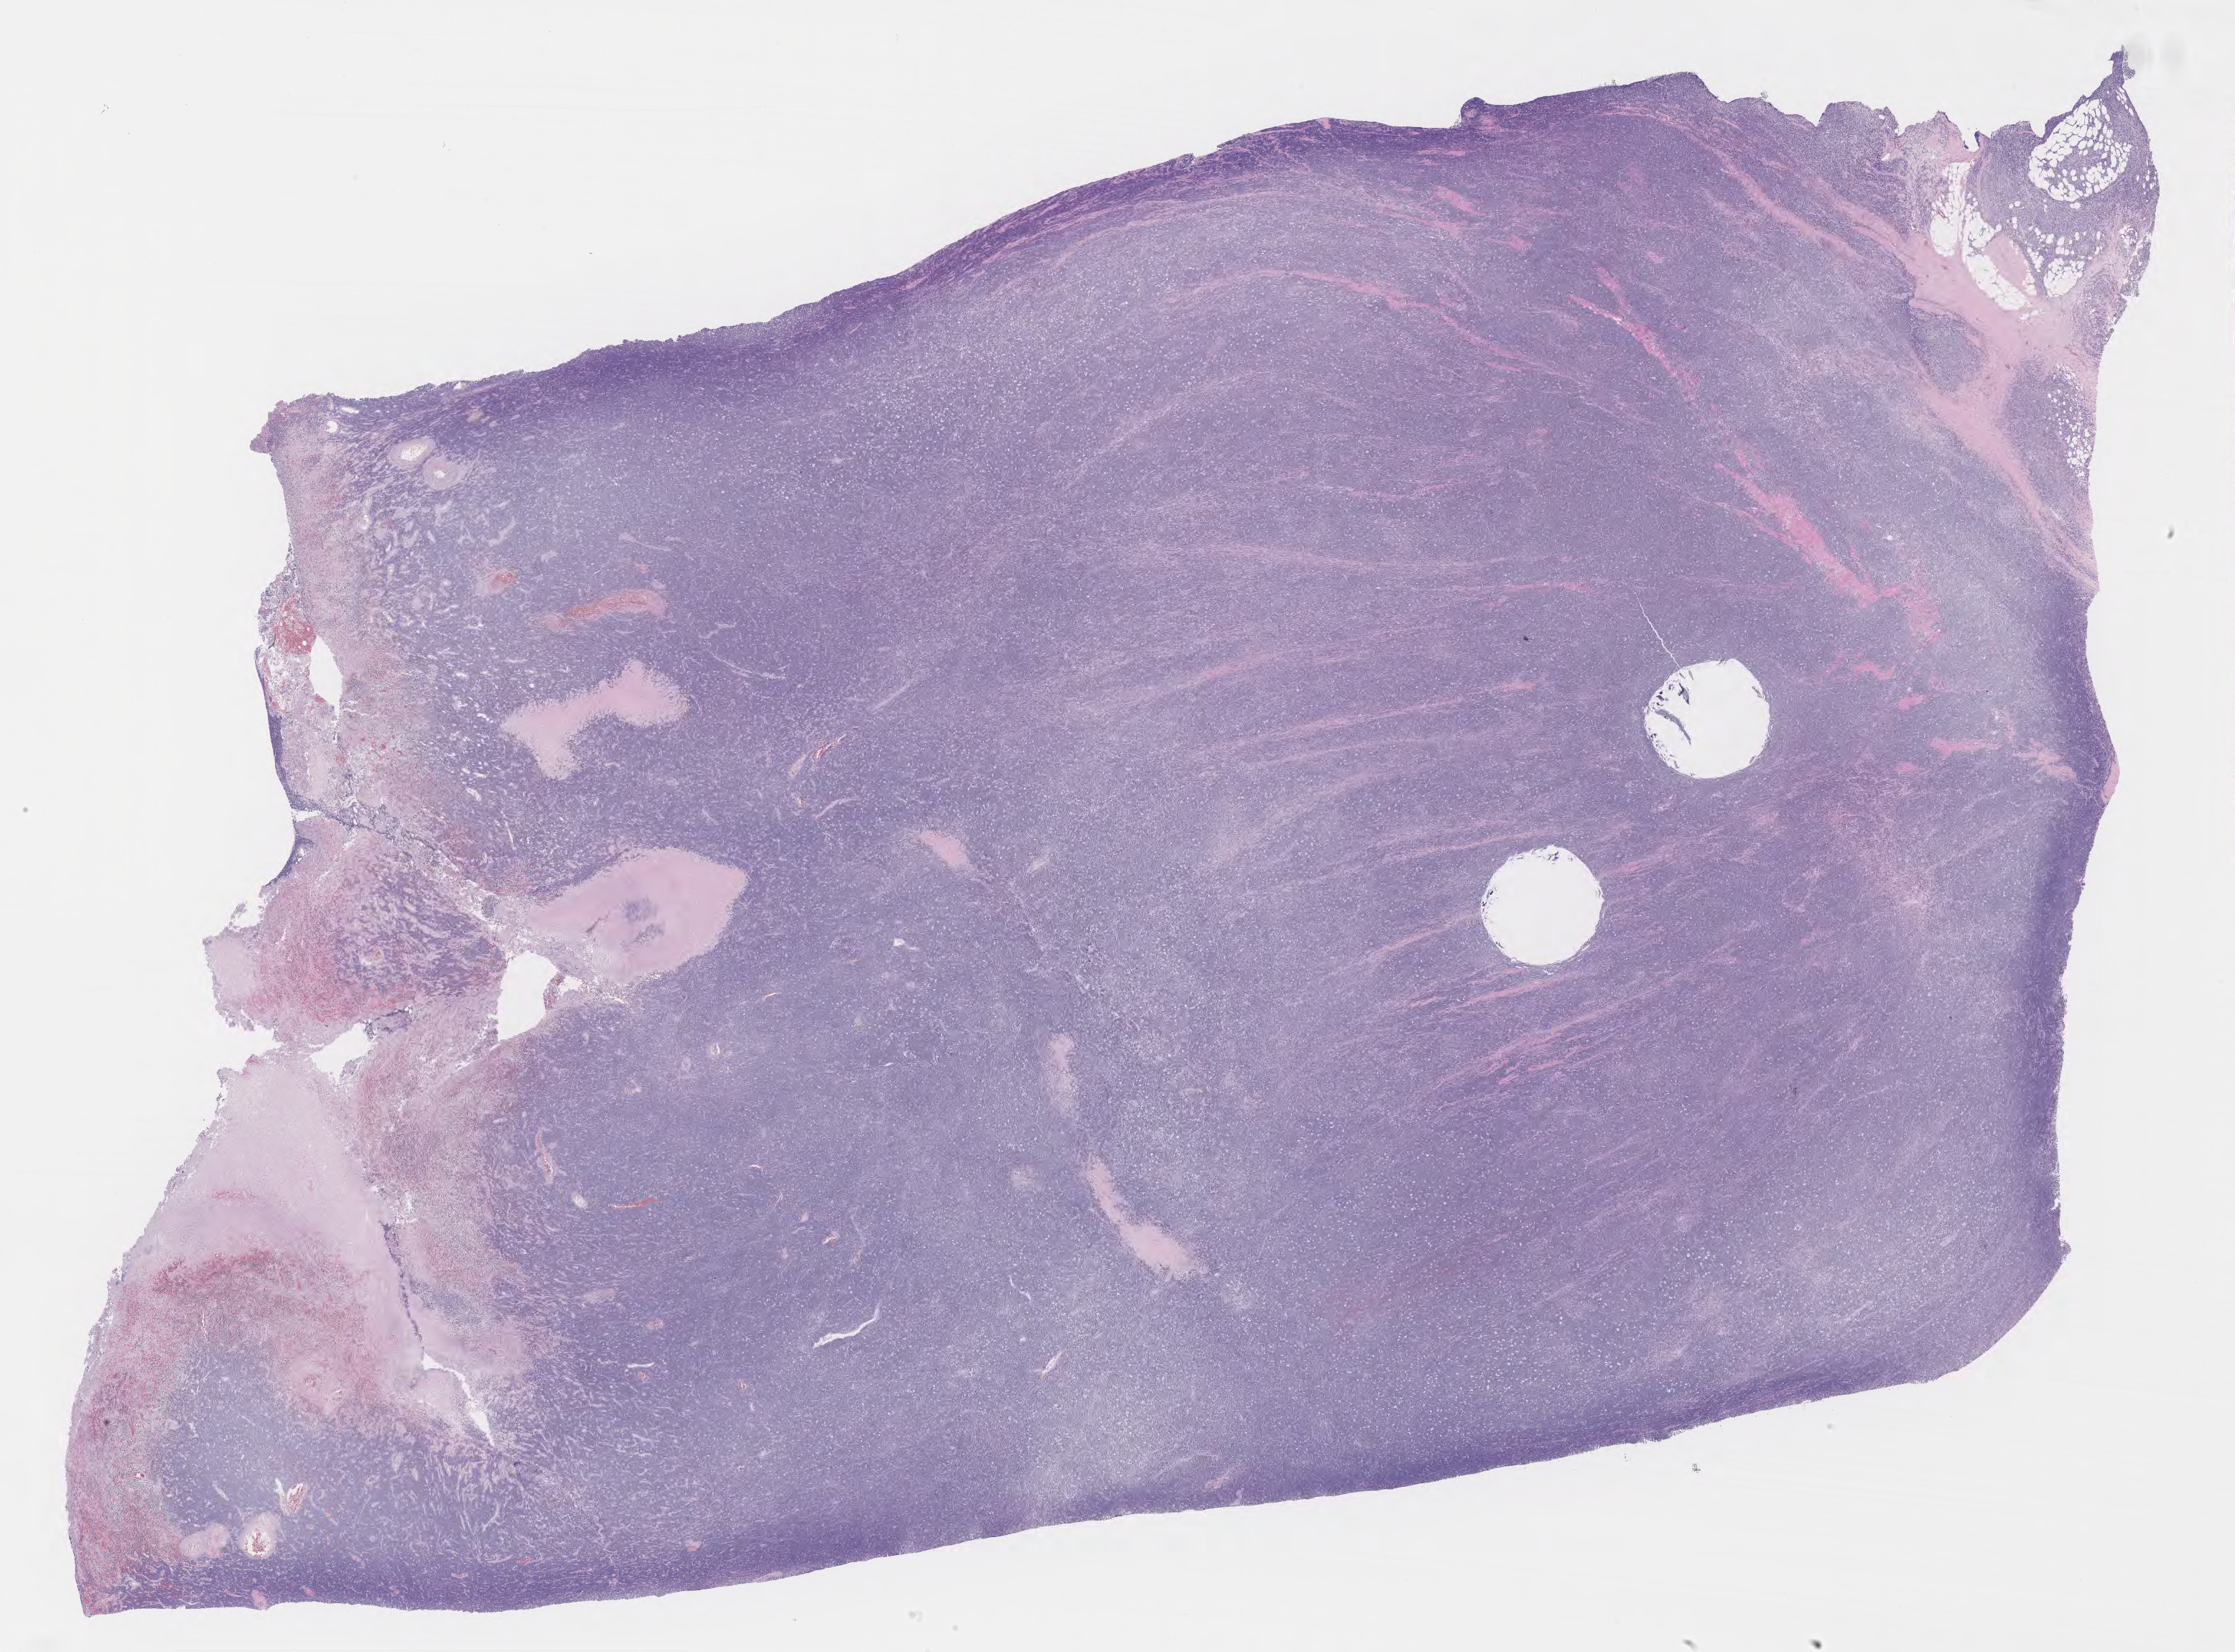
Whole-slide image, H&E stain, low-resolution overview of the scanned area, about 25.2 x 18.6 mm. Specimen: tumor tissue. Site: colon. Patient female; age 59 years.
- histologic diagnosis: Burkitt lymphoma, NOS